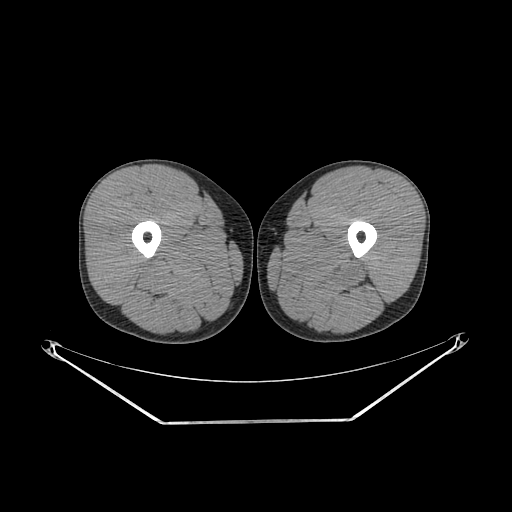
CT of an extremity soft-tissue mass (from a PET/CT study), one axial slice. Position 234 of 267 along the scan axis. Reconstruction kernel SOFT. 140 kVp. Soft-tissue window (W 400 / L 40 HU). 3.75 mm slice thickness. 512 × 512 image matrix, field of view 500 × 500 mm. Male patient. Case-level facts recorded for this patient, not image findings: histological type: extraskeletal osteosarcoma; grade: high; site of the primary tumour: left adductur.
Structures marked on this image (expert contour drawn on MRI and transferred to this co-registered scan by the dataset authors):
- gross tumour volume (mass): bounding box <276,242,380,296> (left, top, right, bottom; pixels)